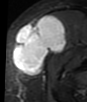
MRI of an extremity soft-tissue mass, one axial slice; STIR; MR volume resampled by the dataset authors to the PET/CT grid (not the native acquisition matrix); 3.27 mm slice thickness; 87 × 102 image matrix, field of view 85 × 100 mm. Female patient. From the clinical record (not read from this slice): histological type: synovial sarcoma; grade: intermediate; site of the primary tumour: right thigh.
Structures marked on this image (expert contour drawn on MRI and transferred to this co-registered scan by the dataset authors):
- gross tumour volume including surrounding oedema: bounding box [x1, y1, x2, y2] px = [13, 15, 68, 76]
- gross tumour volume (mass): [13, 15, 68, 76]